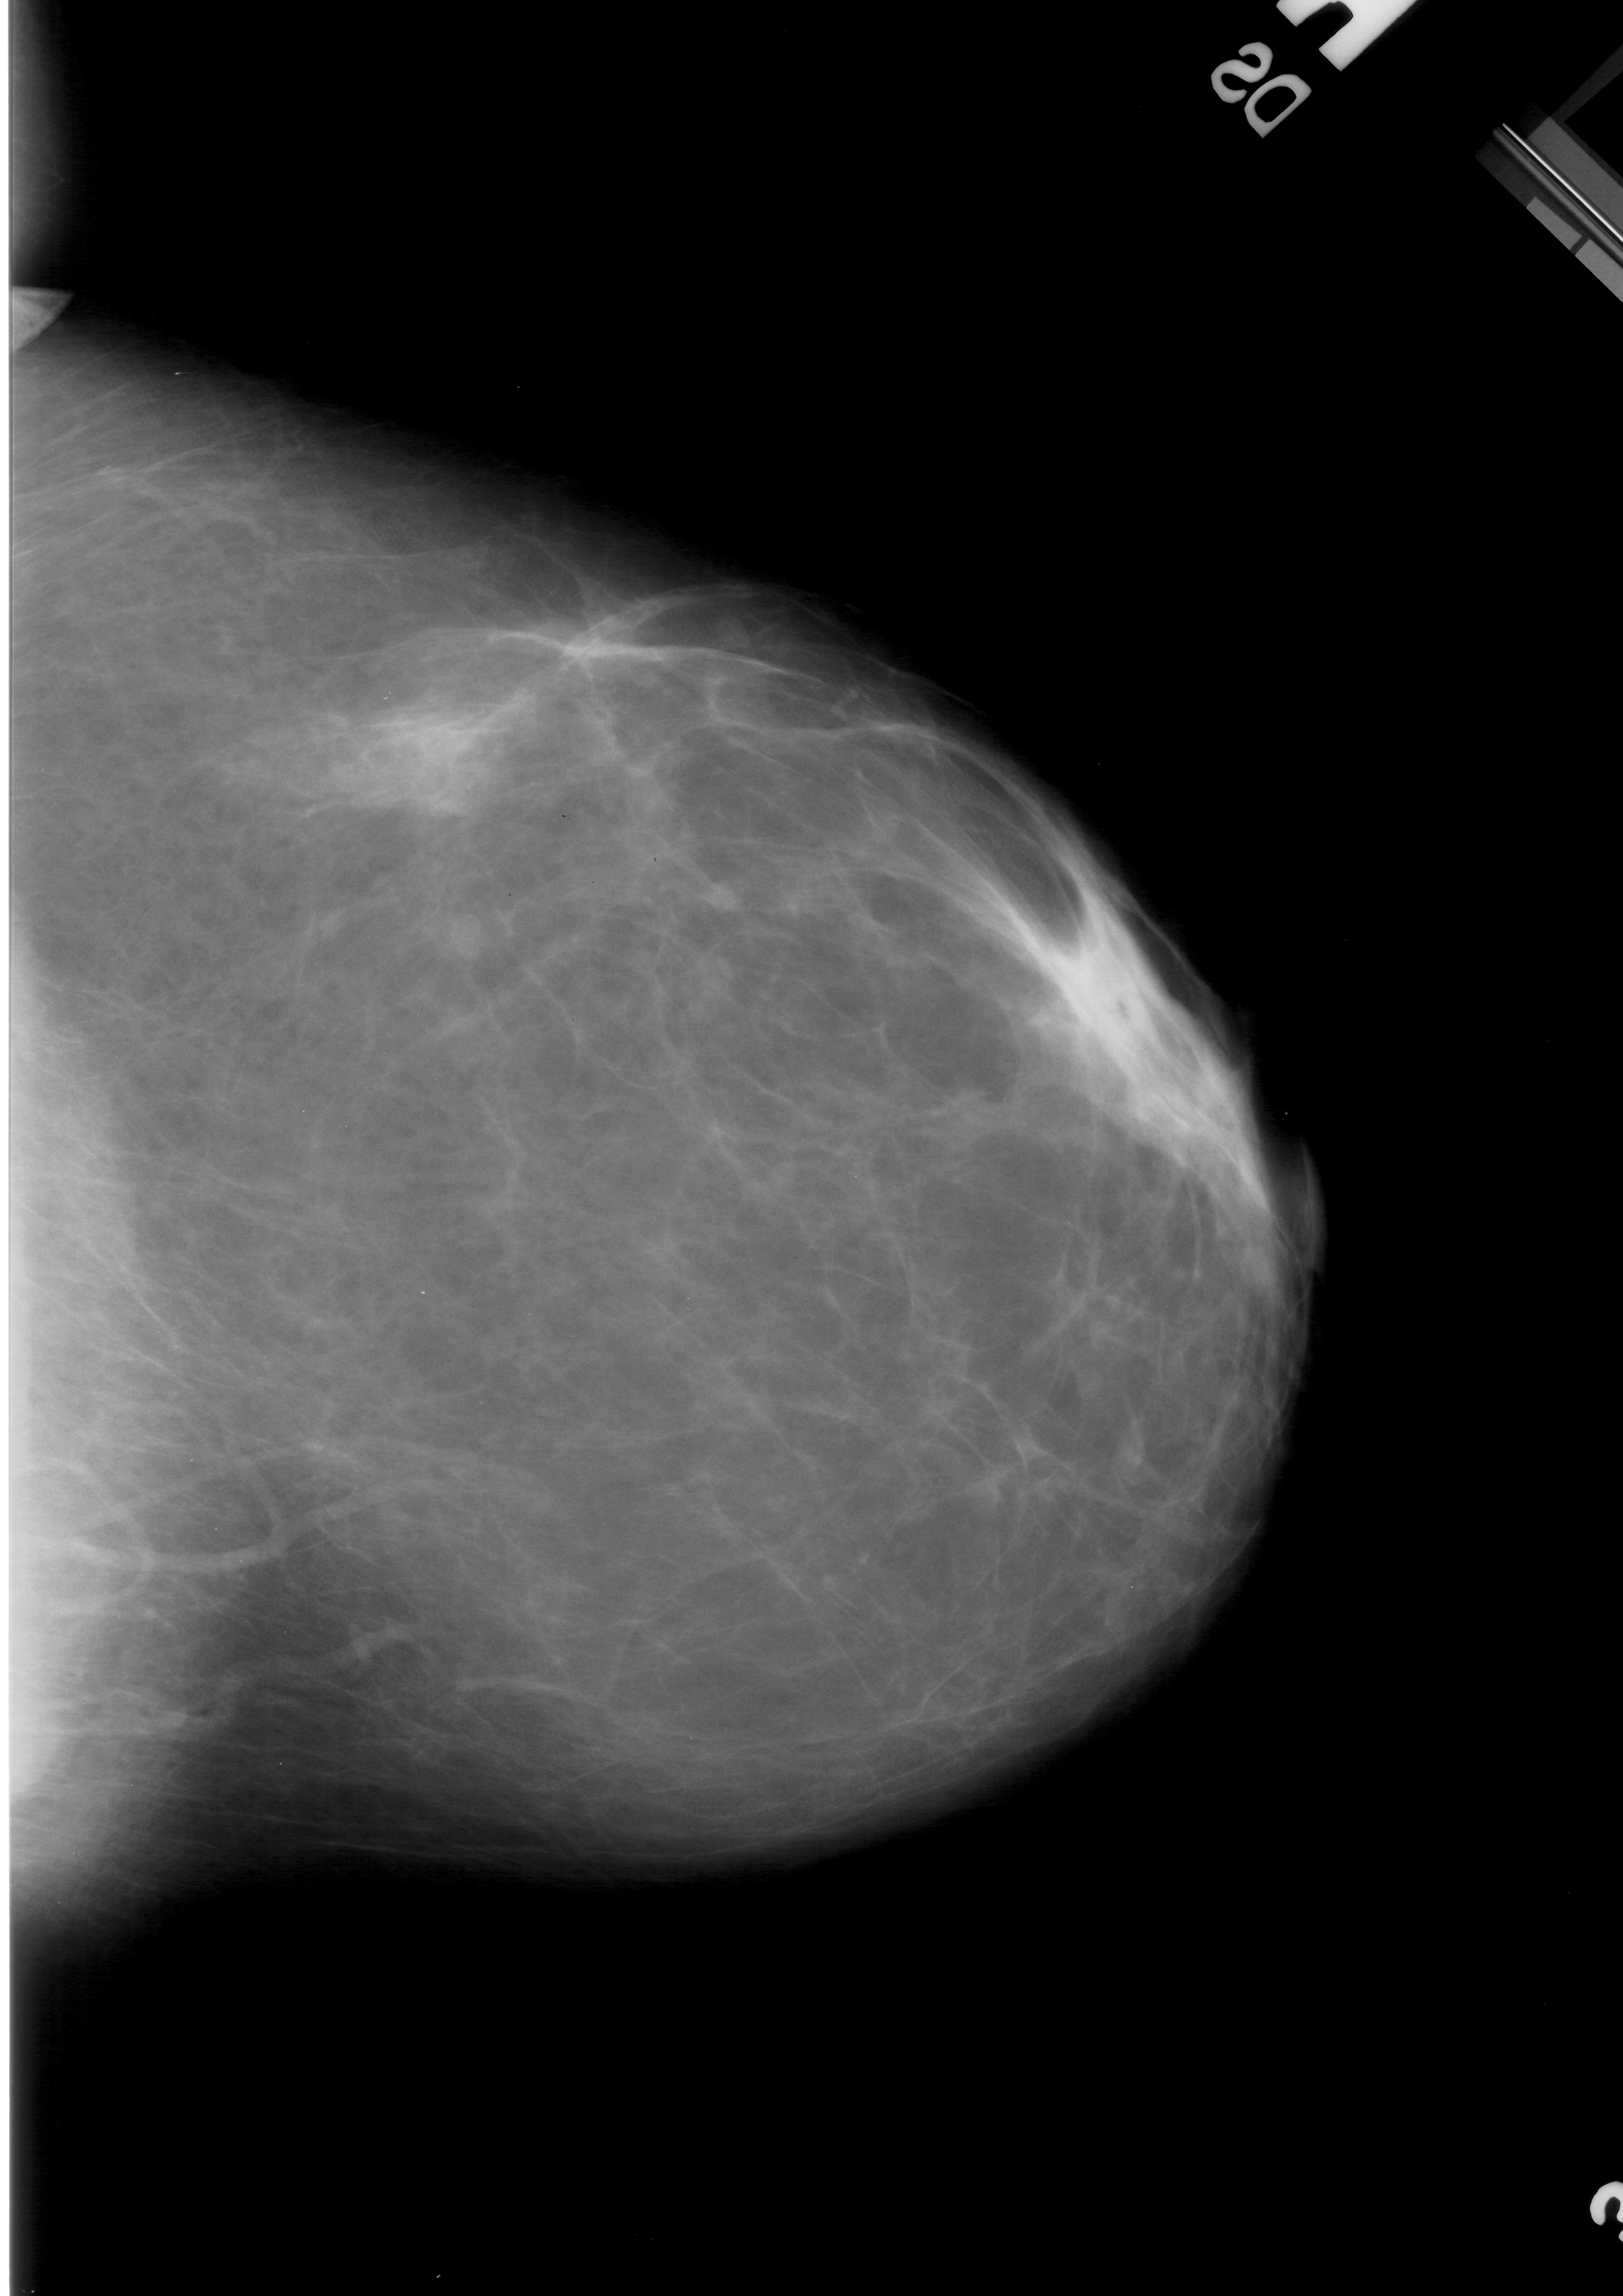
Mammogram (digitized film), right breast, CC view, BI-RADS breast density category 1 (scale 1–4).
Abnormality record for this image: mass, shape lobulated, margins obscured; BI-RADS assessment category 3; pathology result (as recorded, not read from the image): benign.